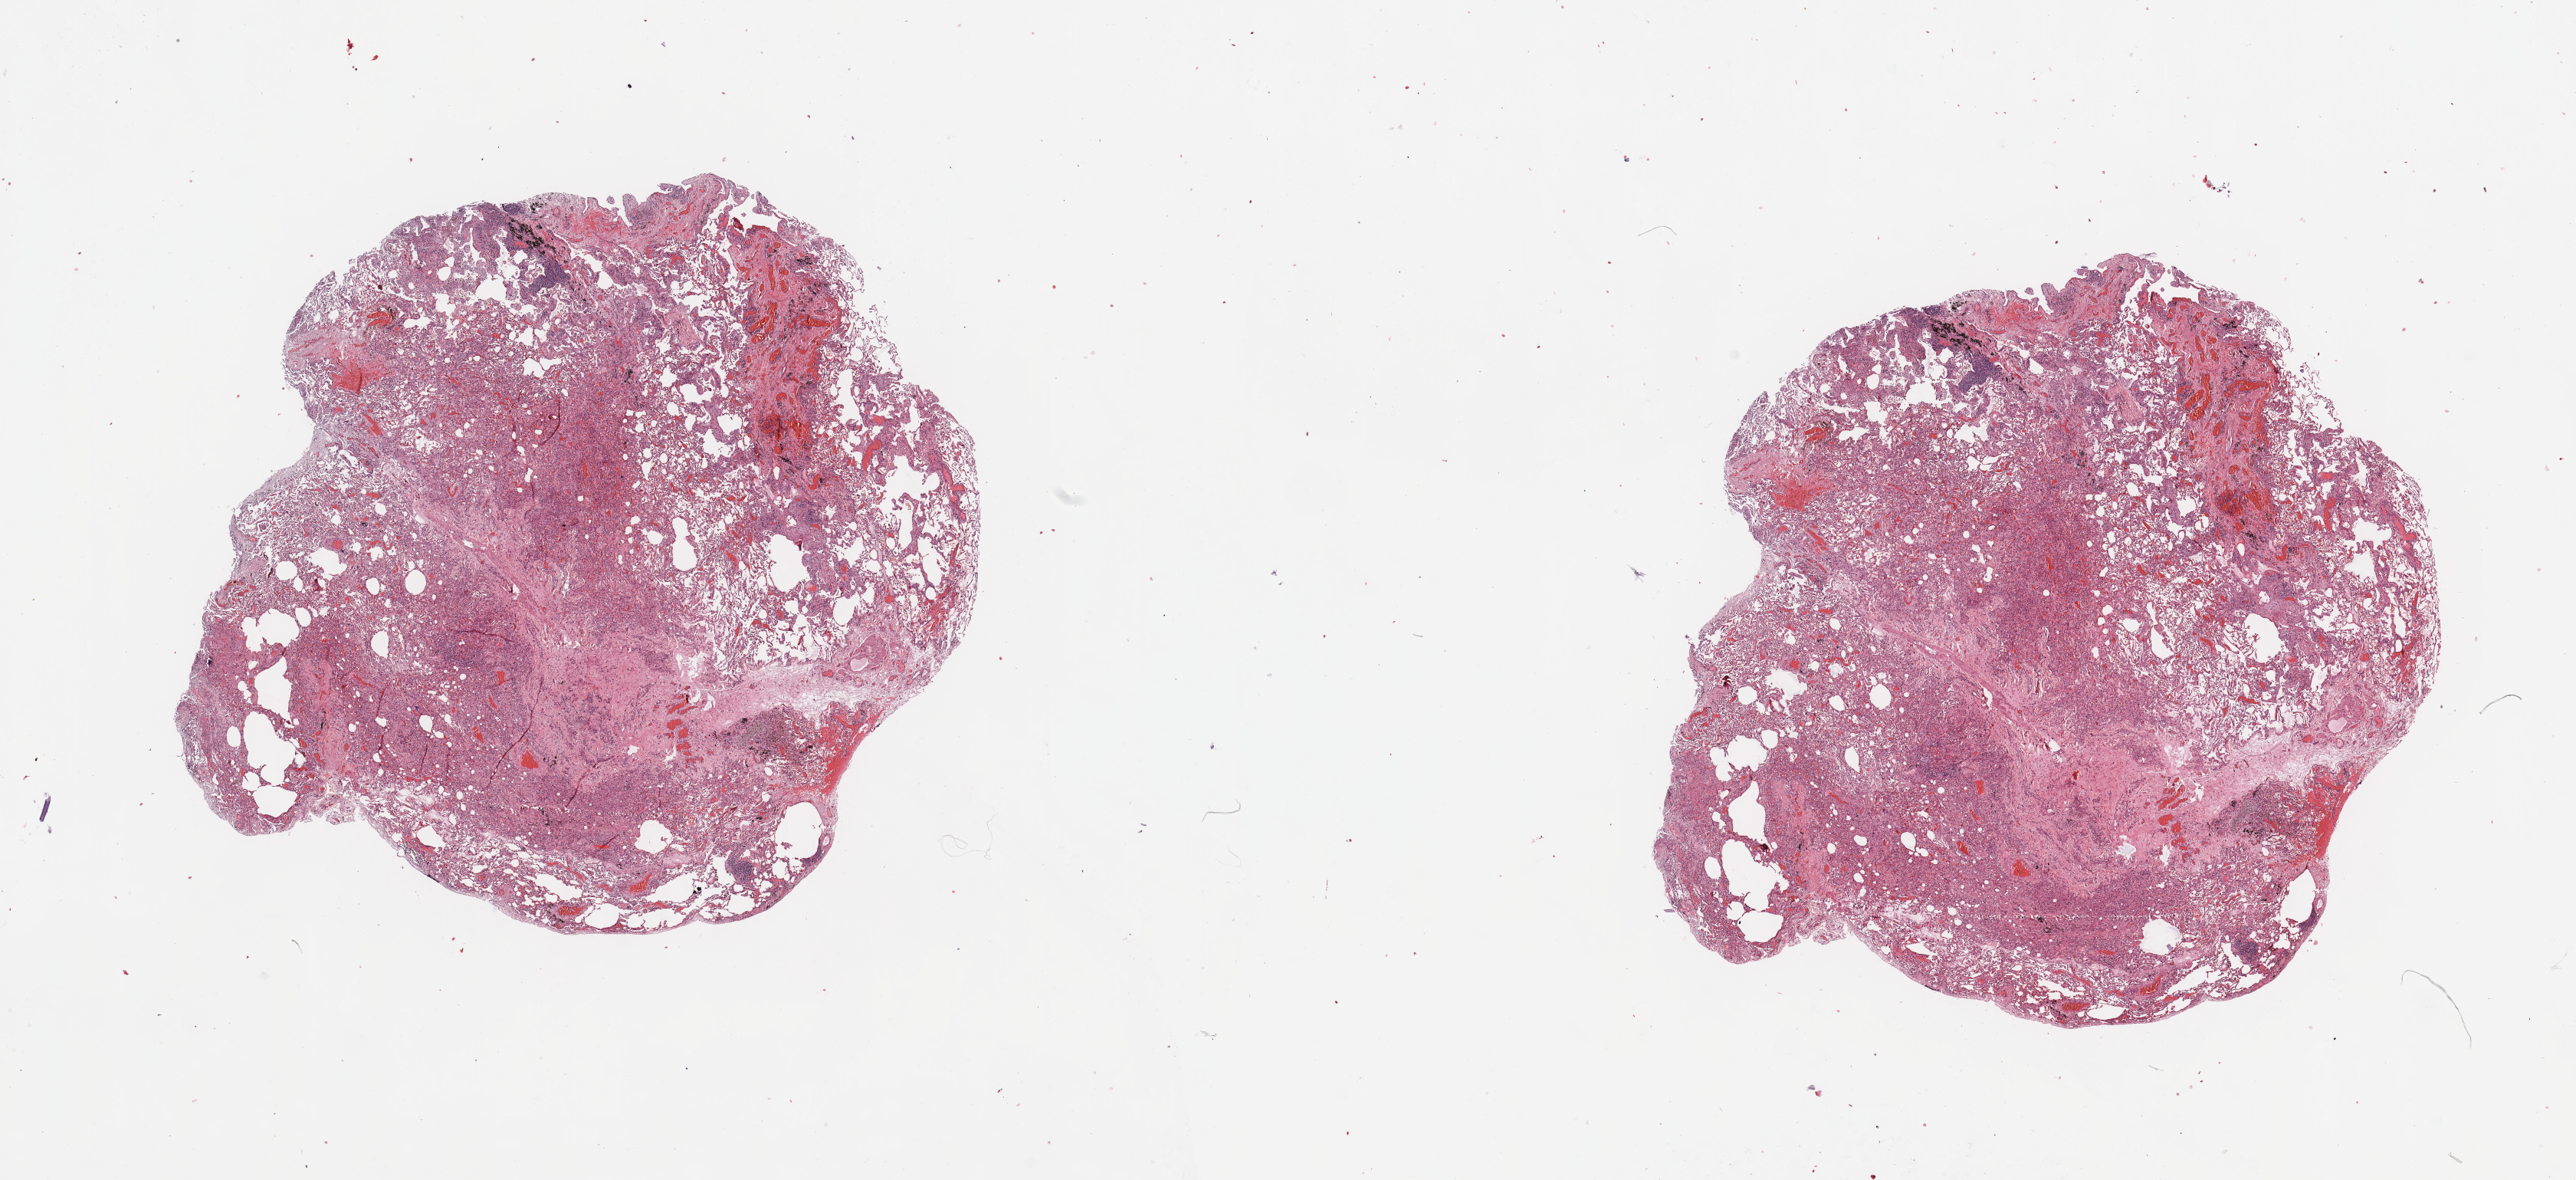
H&E whole-slide image, whole scanned area (about 26.6 x 12.2 mm) shown as a low-resolution overview. Lung, normal (non-tumour) tissue. Male, 61 y/o.
This section: normal (non-tumour) tissue from the same patient. Patient diagnosis: Squamous cell carcinoma, NOS.